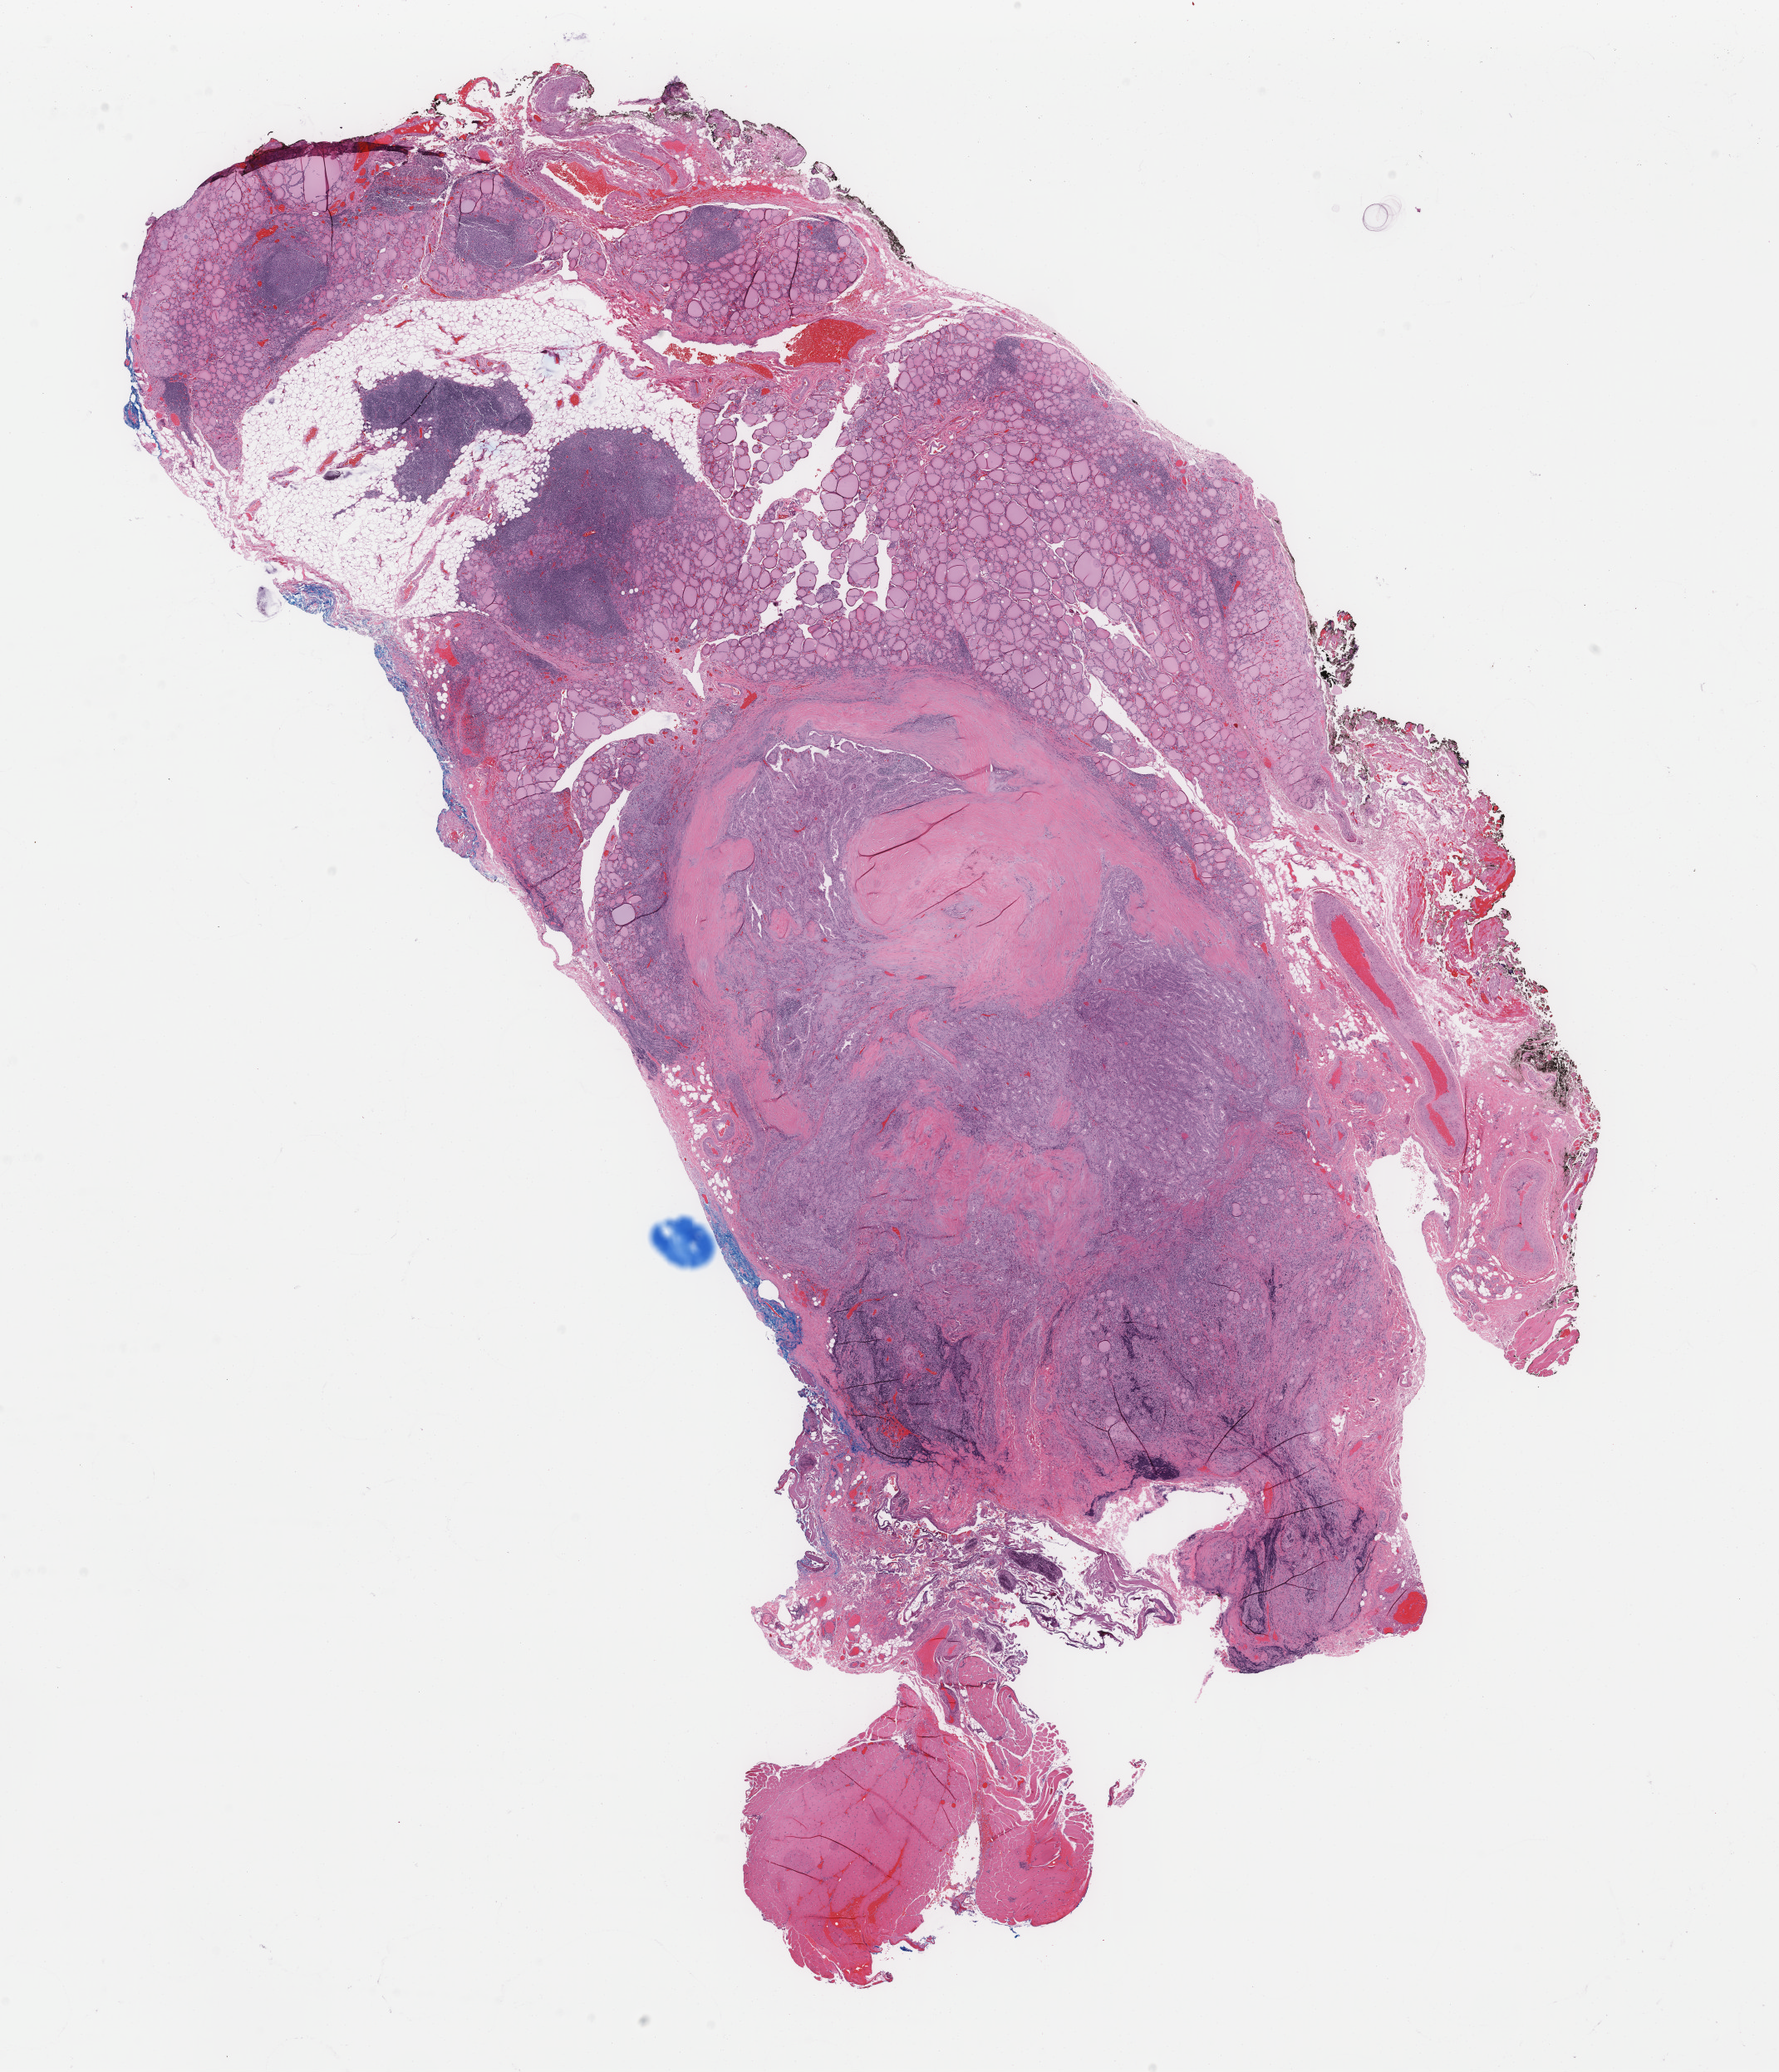
Whole-slide histology image, H&E-stained — whole scanned area (about 17.0 x 19.8 mm) shown as a low-resolution overview, formalin-fixed paraffin-embedded (FFPE) diagnostic section, primary tumour sample from the thyroid. Female, age 61 years at initial diagnosis.
AJCC pathologic stage: III. Histologic diagnosis: Papillary carcinoma, columnar cell (thyroid gland). TNM: T3 N1a M0. Laterality: left.